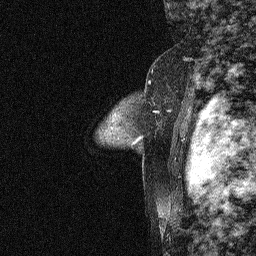
Breast MRI (dynamic contrast-enhanced), one sagittal slice. Slice 49 of 64 in the series (ordered by position). Dynamic contrast-enhanced study with each time point stored as its own series, time point 2 of 3 at this slice position (early post-contrast, ordered by acquisition time). 1.5 T. TE 4.5 ms, TR 11 ms. 2.06 mm slice thickness. 256 × 256 image matrix, field of view 200 × 200 mm. Patient: female, 46 years. From the clinical record (not read from this slice): setting: breast cancer imaged before/during neoadjuvant chemotherapy; receptor status: HER2-positive.
Annotated regions visible in this slice (semi-automatically segmented with operator editing):
- analysis volume of interest (the breast-tissue region the enhancement analysis was run in; not a lesion): bounding box <46,51,180,169> (left, top, right, bottom; pixels)
- tumour enhancement mask (voxels above the 90 % enhancement threshold inside the analysis volume of interest): <154,110,170,112>